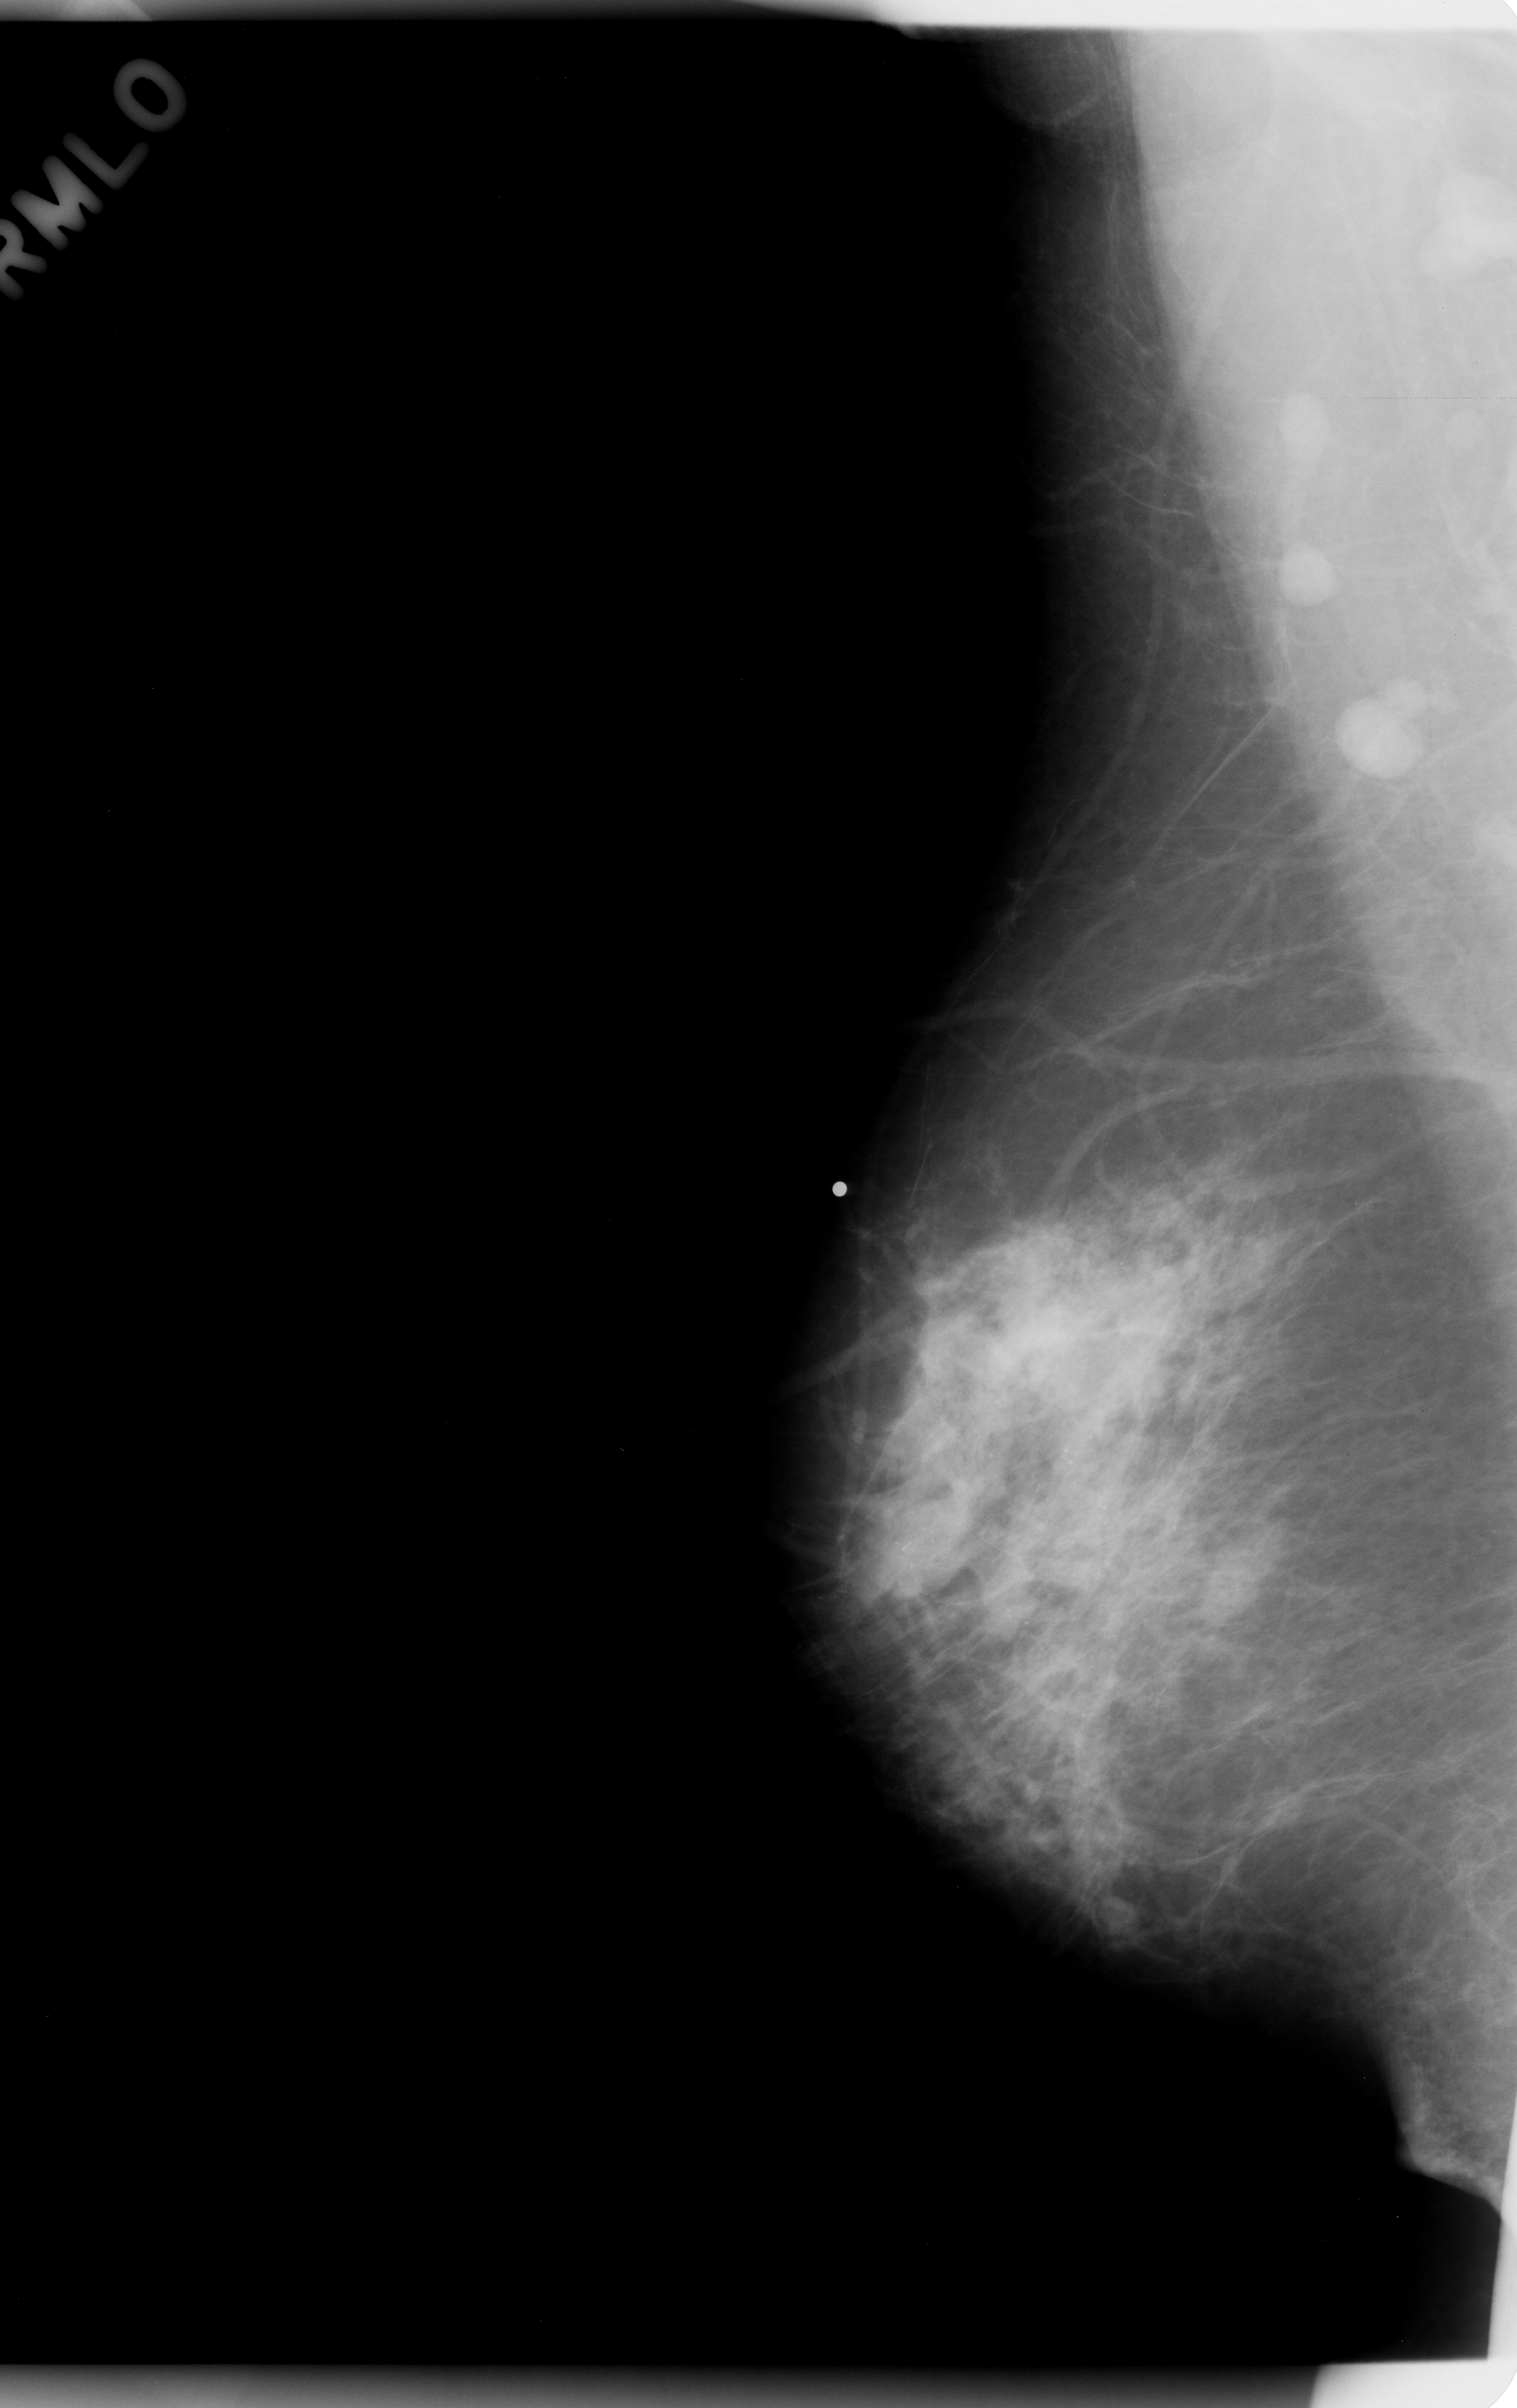
Mammogram (digitized film). Right breast. Mediolateral oblique (MLO) view. BI-RADS breast density category 2 (scale 1–4). 1517 × 2408 image matrix.
Expert-marked regions of interest on this film, with their recorded descriptors:
- calcifications, morphology pleomorphic, distribution regional; BI-RADS assessment category 5; pathology result (as recorded, not read from the image): malignant: box from (x=803, y=917) to (x=1411, y=1962) px